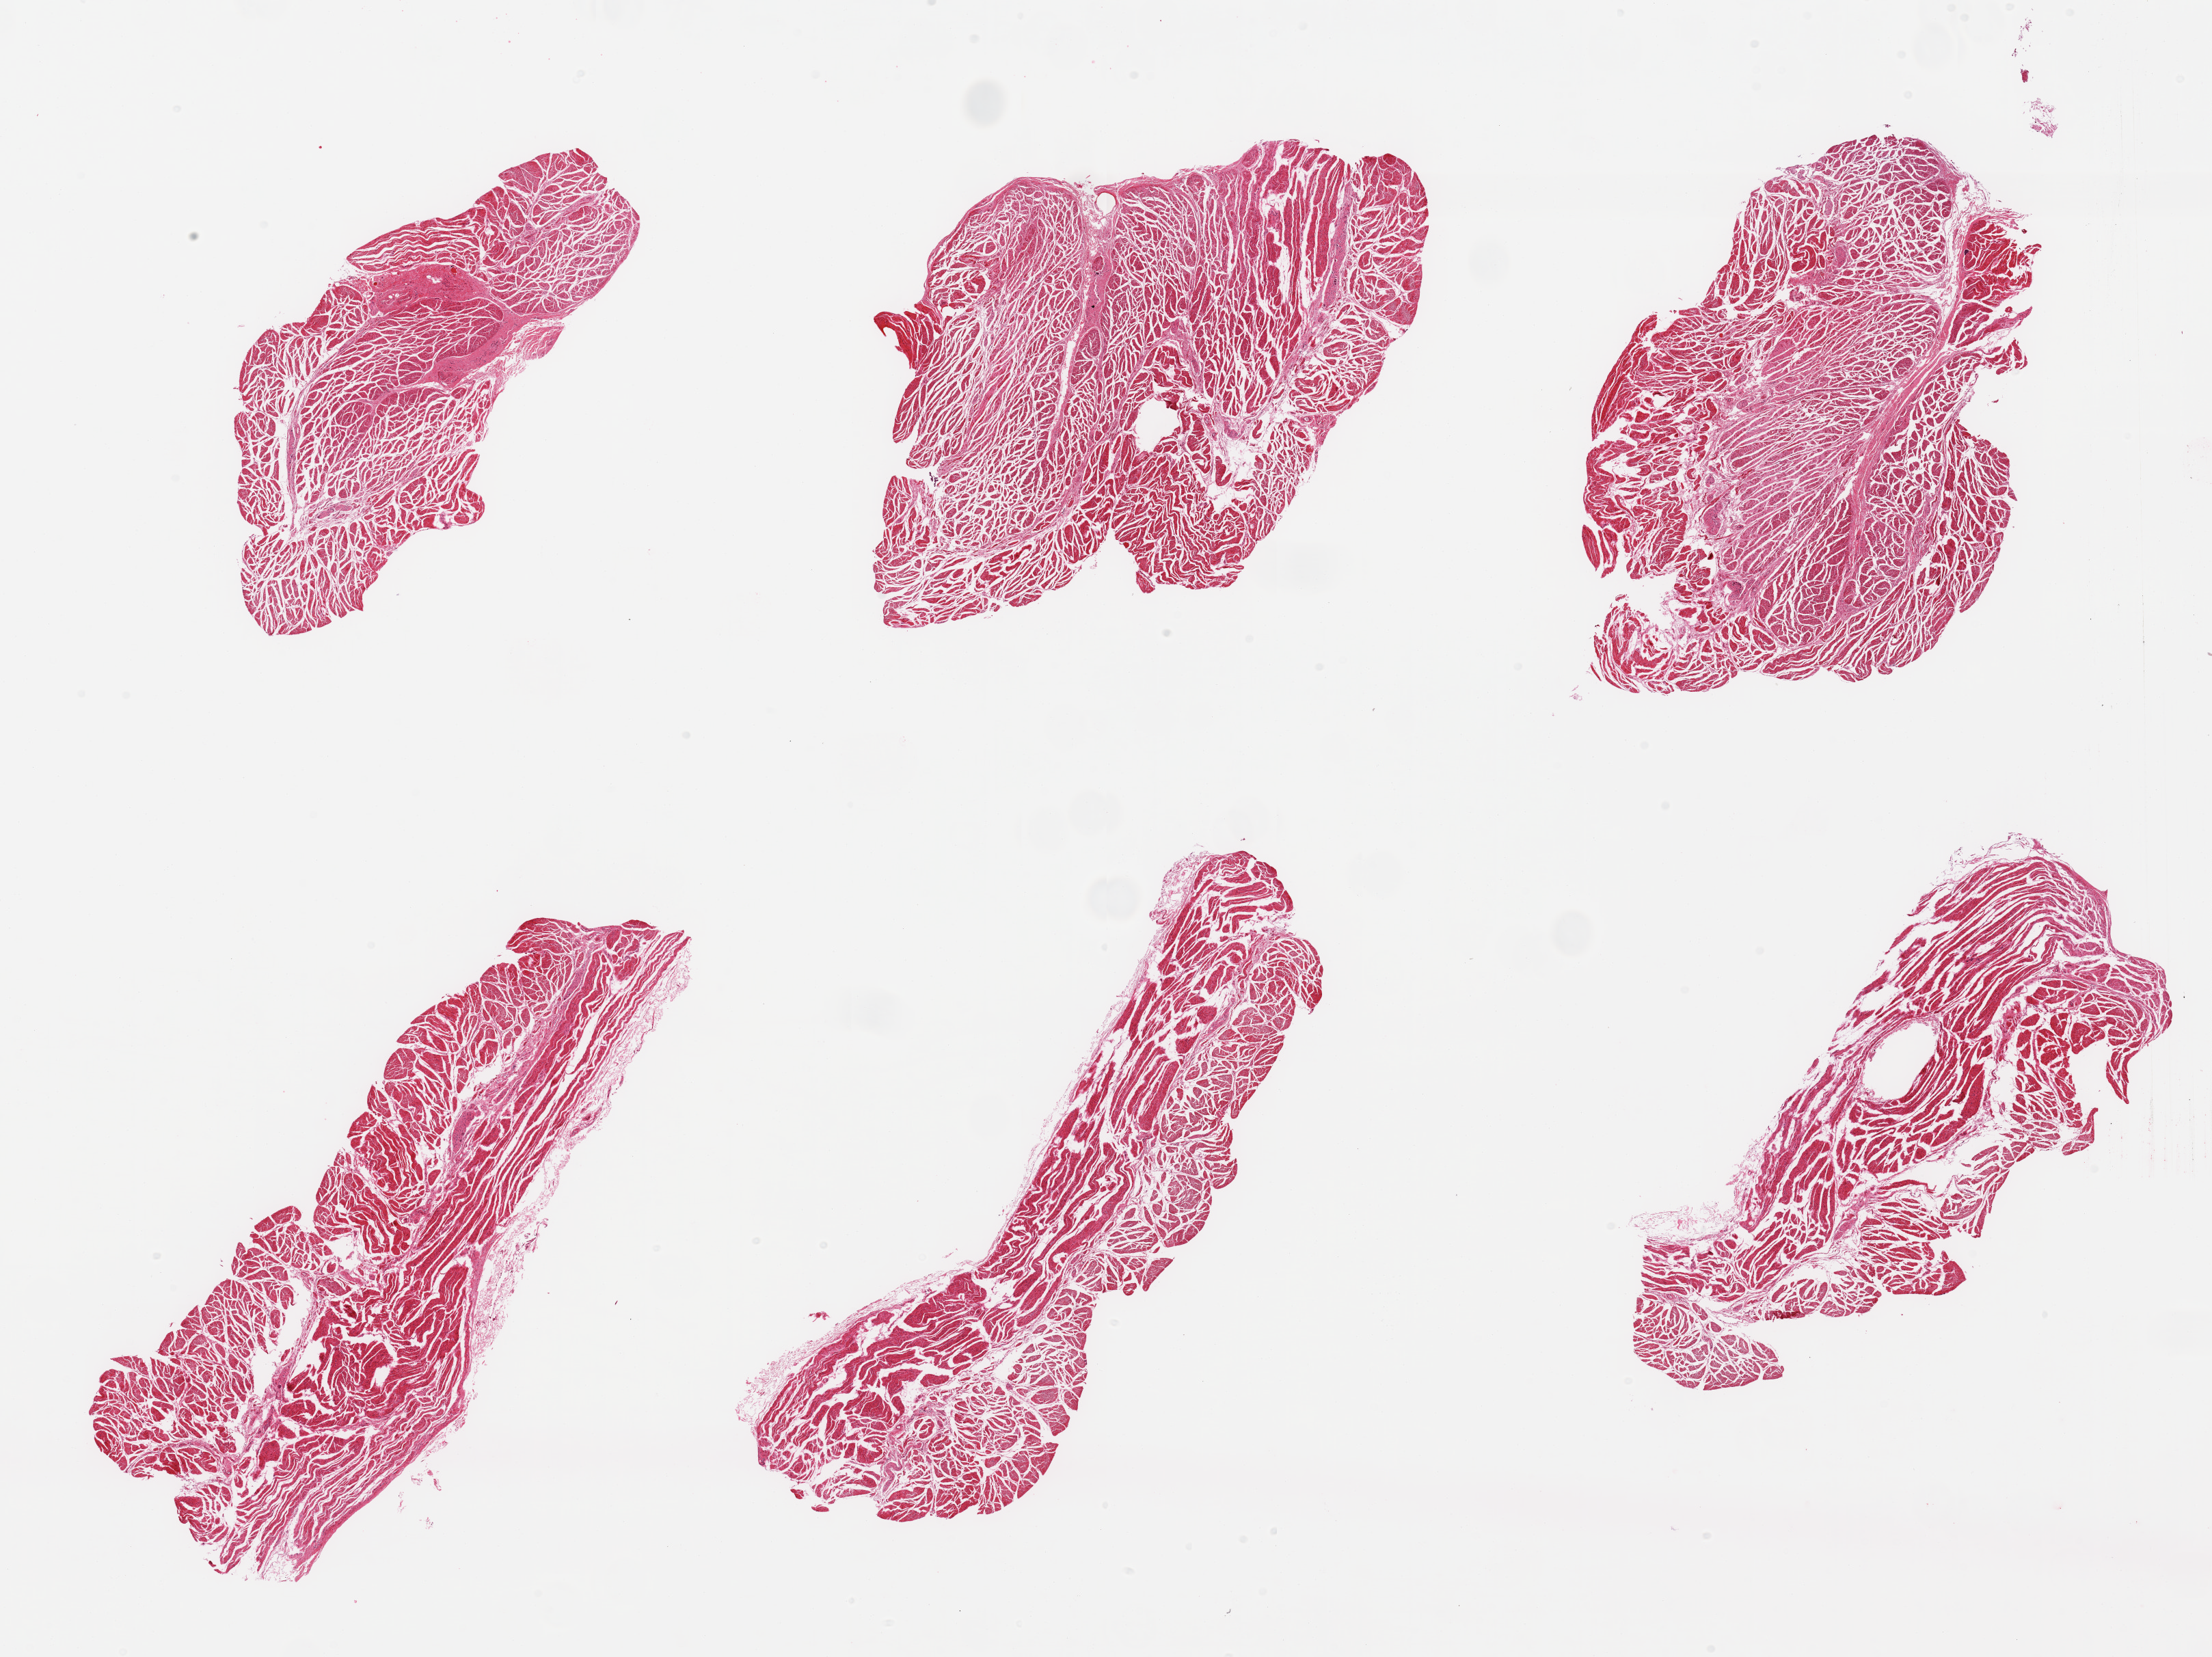
Digitized haematoxylin and eosin-stained section, brightfield — low-resolution overview of the scanned area, about 25.6 x 19.2 mm. PAXgene-fixed, paraffin-embedded tissue. Section of esophageal muscle (target tissue). Tissue donor sample. Donor sex: male.
Review note (as recorded): 6 pieces; foci of interstitial fibrosis consistent with scleroderma.